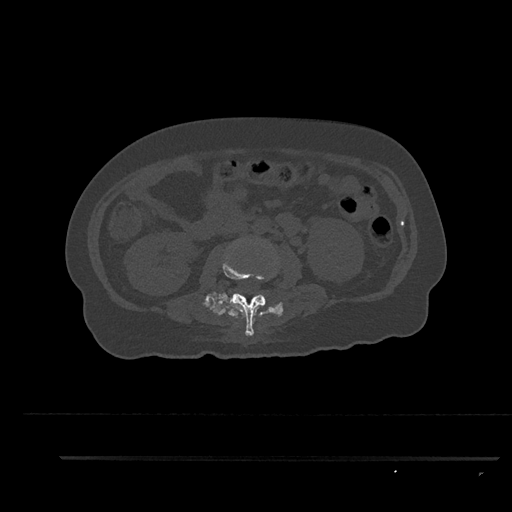
CT including the spine, one axial slice; slice 132 of 797 in the series (ordered by position); reconstruction kernel Br40s/3; bone window (W 1800 / L 400 HU); 0.5 mm slice thickness; 512 × 512 image matrix. Female patient, age 44 years. Case-level facts recorded for this patient, not image findings: primary cancer: renal; vertebrae with lytic lesions (as recorded): L1.
Outlined on this slice (semi-automatic segmentation, software-assisted and operator-edited):
- L2 vertebra: box from (x=223, y=260) to (x=266, y=336) px
- L3 vertebra: (x=264, y=297)–(x=266, y=301)